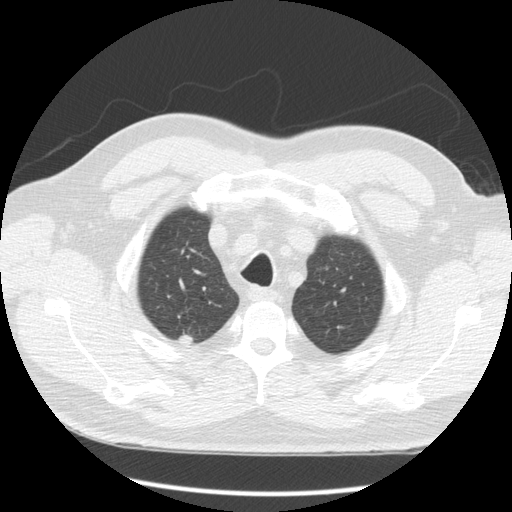
Chest CT (low-dose screening protocol), one axial image, baseline annual screen, lung window (W 1500 / L -600 HU), 2.5 mm slice thickness, standard (soft-tissue) reconstruction kernel (STANDARD), 120 kVp, 512 × 512 image matrix, field of view 360 × 360 mm. Male, age 65 years at enrolment. Former smoker at enrolment.
Lesion marked by an expert reader, bounding box (x1, y1, x2, y2) in pixels: (164, 322, 204, 357). Reader record for this screening exam (exam-level; its link to the box is not recorded): non-calcified nodule or mass ≥4 mm, right upper lobe, 10 × 9 mm, spiculated (stellate) margins, soft tissue attenuation. Lung cancer was diagnosed 103 days after this screen: squamous cell carcinoma, NOS, right upper lobe, poorly differentiated (G3), stage IA (AJCC 6th edition), 5 mm at pathology.